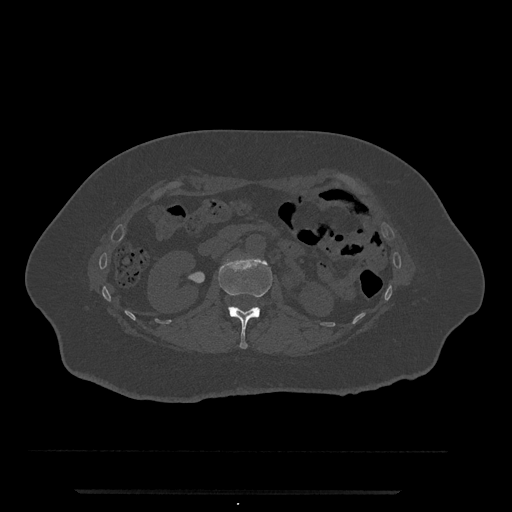
CT including the spine, one axial slice. Position 92 of 797 along the scan axis. Bone window (W 1800 / L 400 HU). 0.5 mm slice thickness. 512 × 512 image matrix. Patient: female, 51 years. From the clinical record (not read from this slice): primary cancer: neuro; vertebrae with lytic lesions (as recorded): T8.
Annotated regions visible in this slice (semi-automatic segmentation, software-assisted and operator-edited):
- L1 vertebra: bounding box (x1, y1, x2, y2) in pixels: (218, 256, 273, 349)
- L2 vertebra: (228, 306, 233, 308)